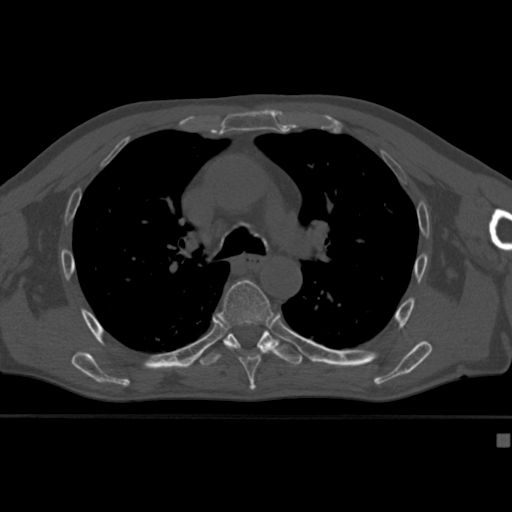
CT including the spine, one axial slice; slice 289 of 430 in the series (ordered by position); reconstruction kernel Br40s; 120 kVp; bone window (W 1800 / L 400 HU); 1.5 mm slice thickness; 512 × 512 image matrix, field of view 337 × 337 mm. Male patient, age 64 years. Case-level facts recorded for this patient, not image findings: primary cancer: uterus.
Annotated regions visible in this slice (semi-automatic segmentation, software-assisted and operator-edited):
- T6 vertebra: bounding box [x1, y1, x2, y2] px = [217, 279, 279, 382]
- T7 vertebra: [199, 330, 303, 368]